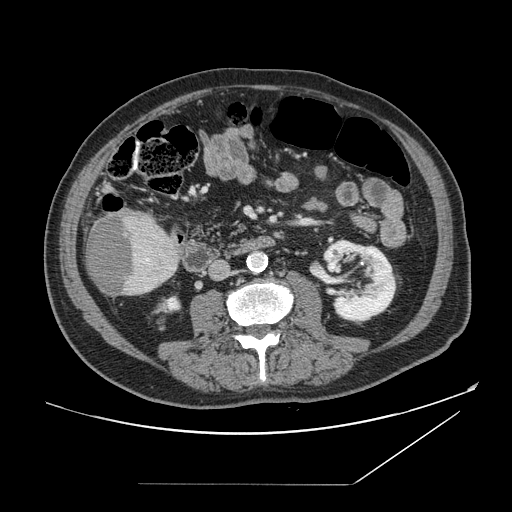
Contrast-enhanced abdominal CT, one axial slice; slice 41 of 166 in the series (ordered by position); 120 kVp; intravenous contrast given; soft-tissue window (W 400 / L 40 HU); 2.5 mm slice thickness; 512 × 512 image matrix, field of view 416 × 416 mm. Male patient, age 80 years. Case-level facts recorded for this patient, not image findings: diagnosis: colorectal cancer liver metastases, imaged before liver resection; multiple liver metastases: no; largest metastasis: 2.2 cm; chemotherapy before resection: no.
Annotated regions visible in this slice (manually delineated by an expert):
- liver: bounding box <87,209,179,296> (left, top, right, bottom; pixels)
- liver metastasis: <87,213,135,293>